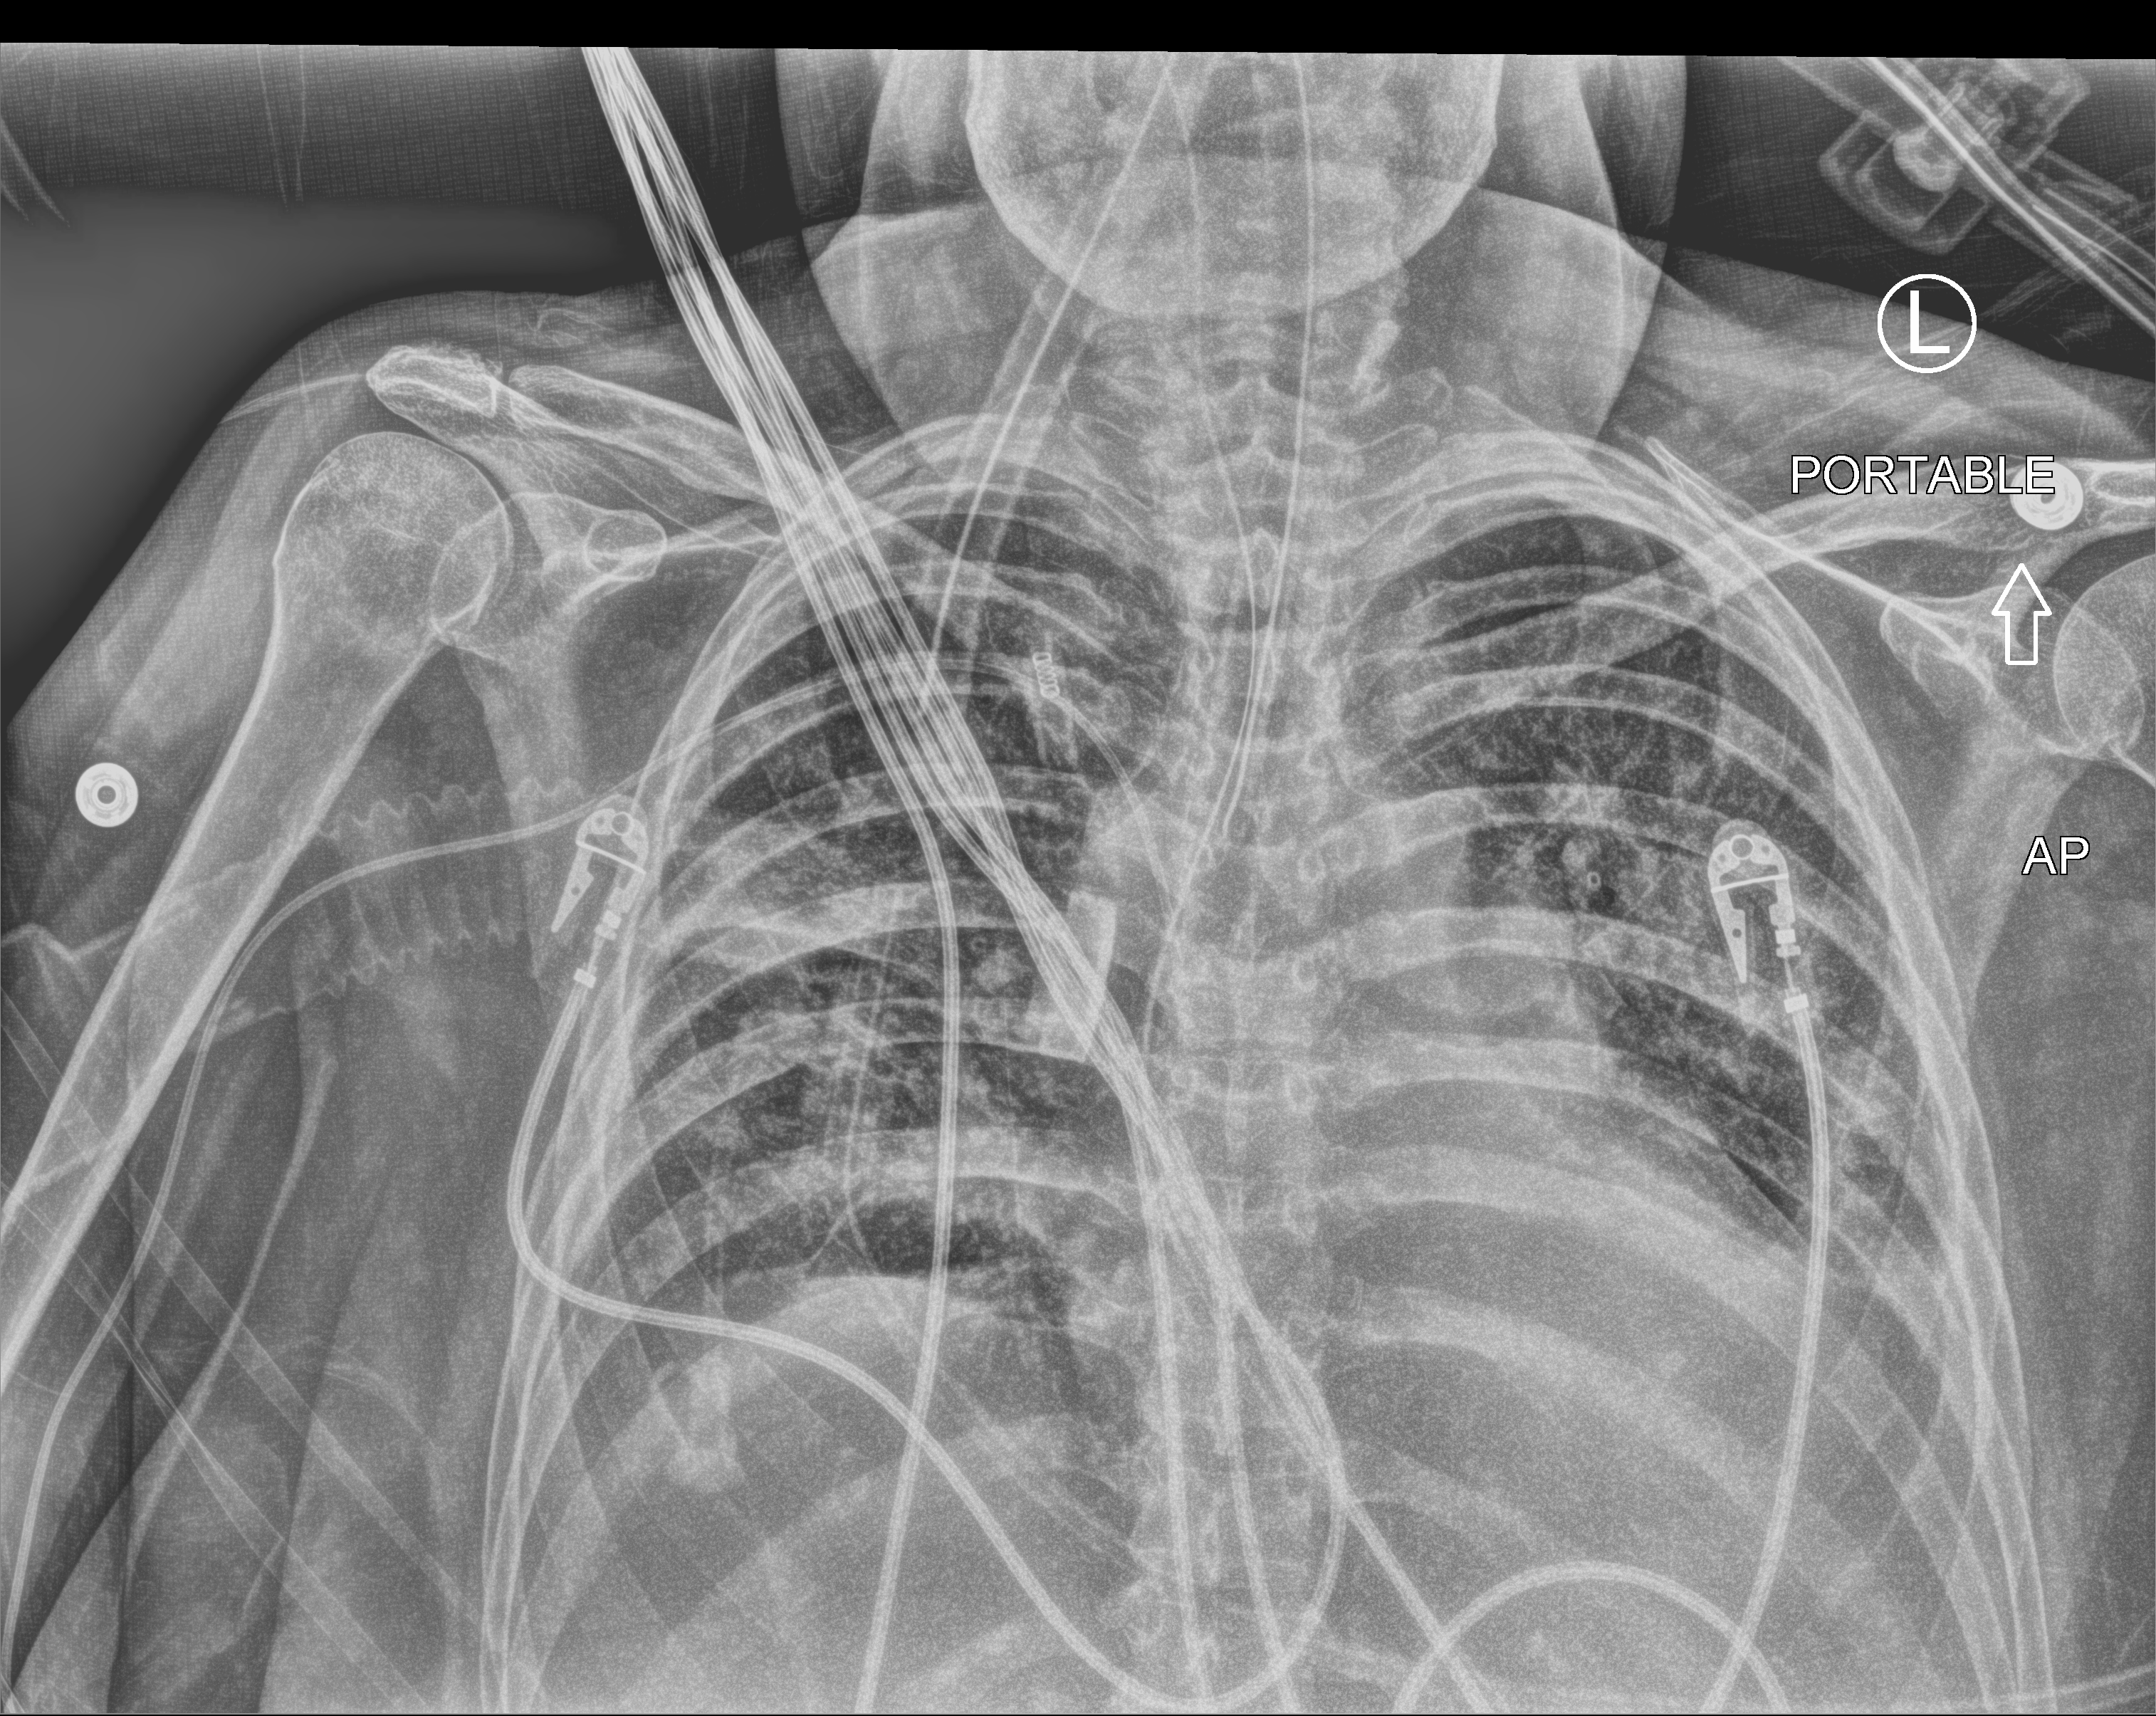
Portable chest radiograph, anteroposterior (AP) projection. Patient hospitalised with COVID-19; female, aged 60–74 years.
From the hospital-stay record, not from the radiograph (when in the stay this image was taken is not recorded):
- length of hospital stay: 9 days
- admitted to intensive care during this hospital stay: yes